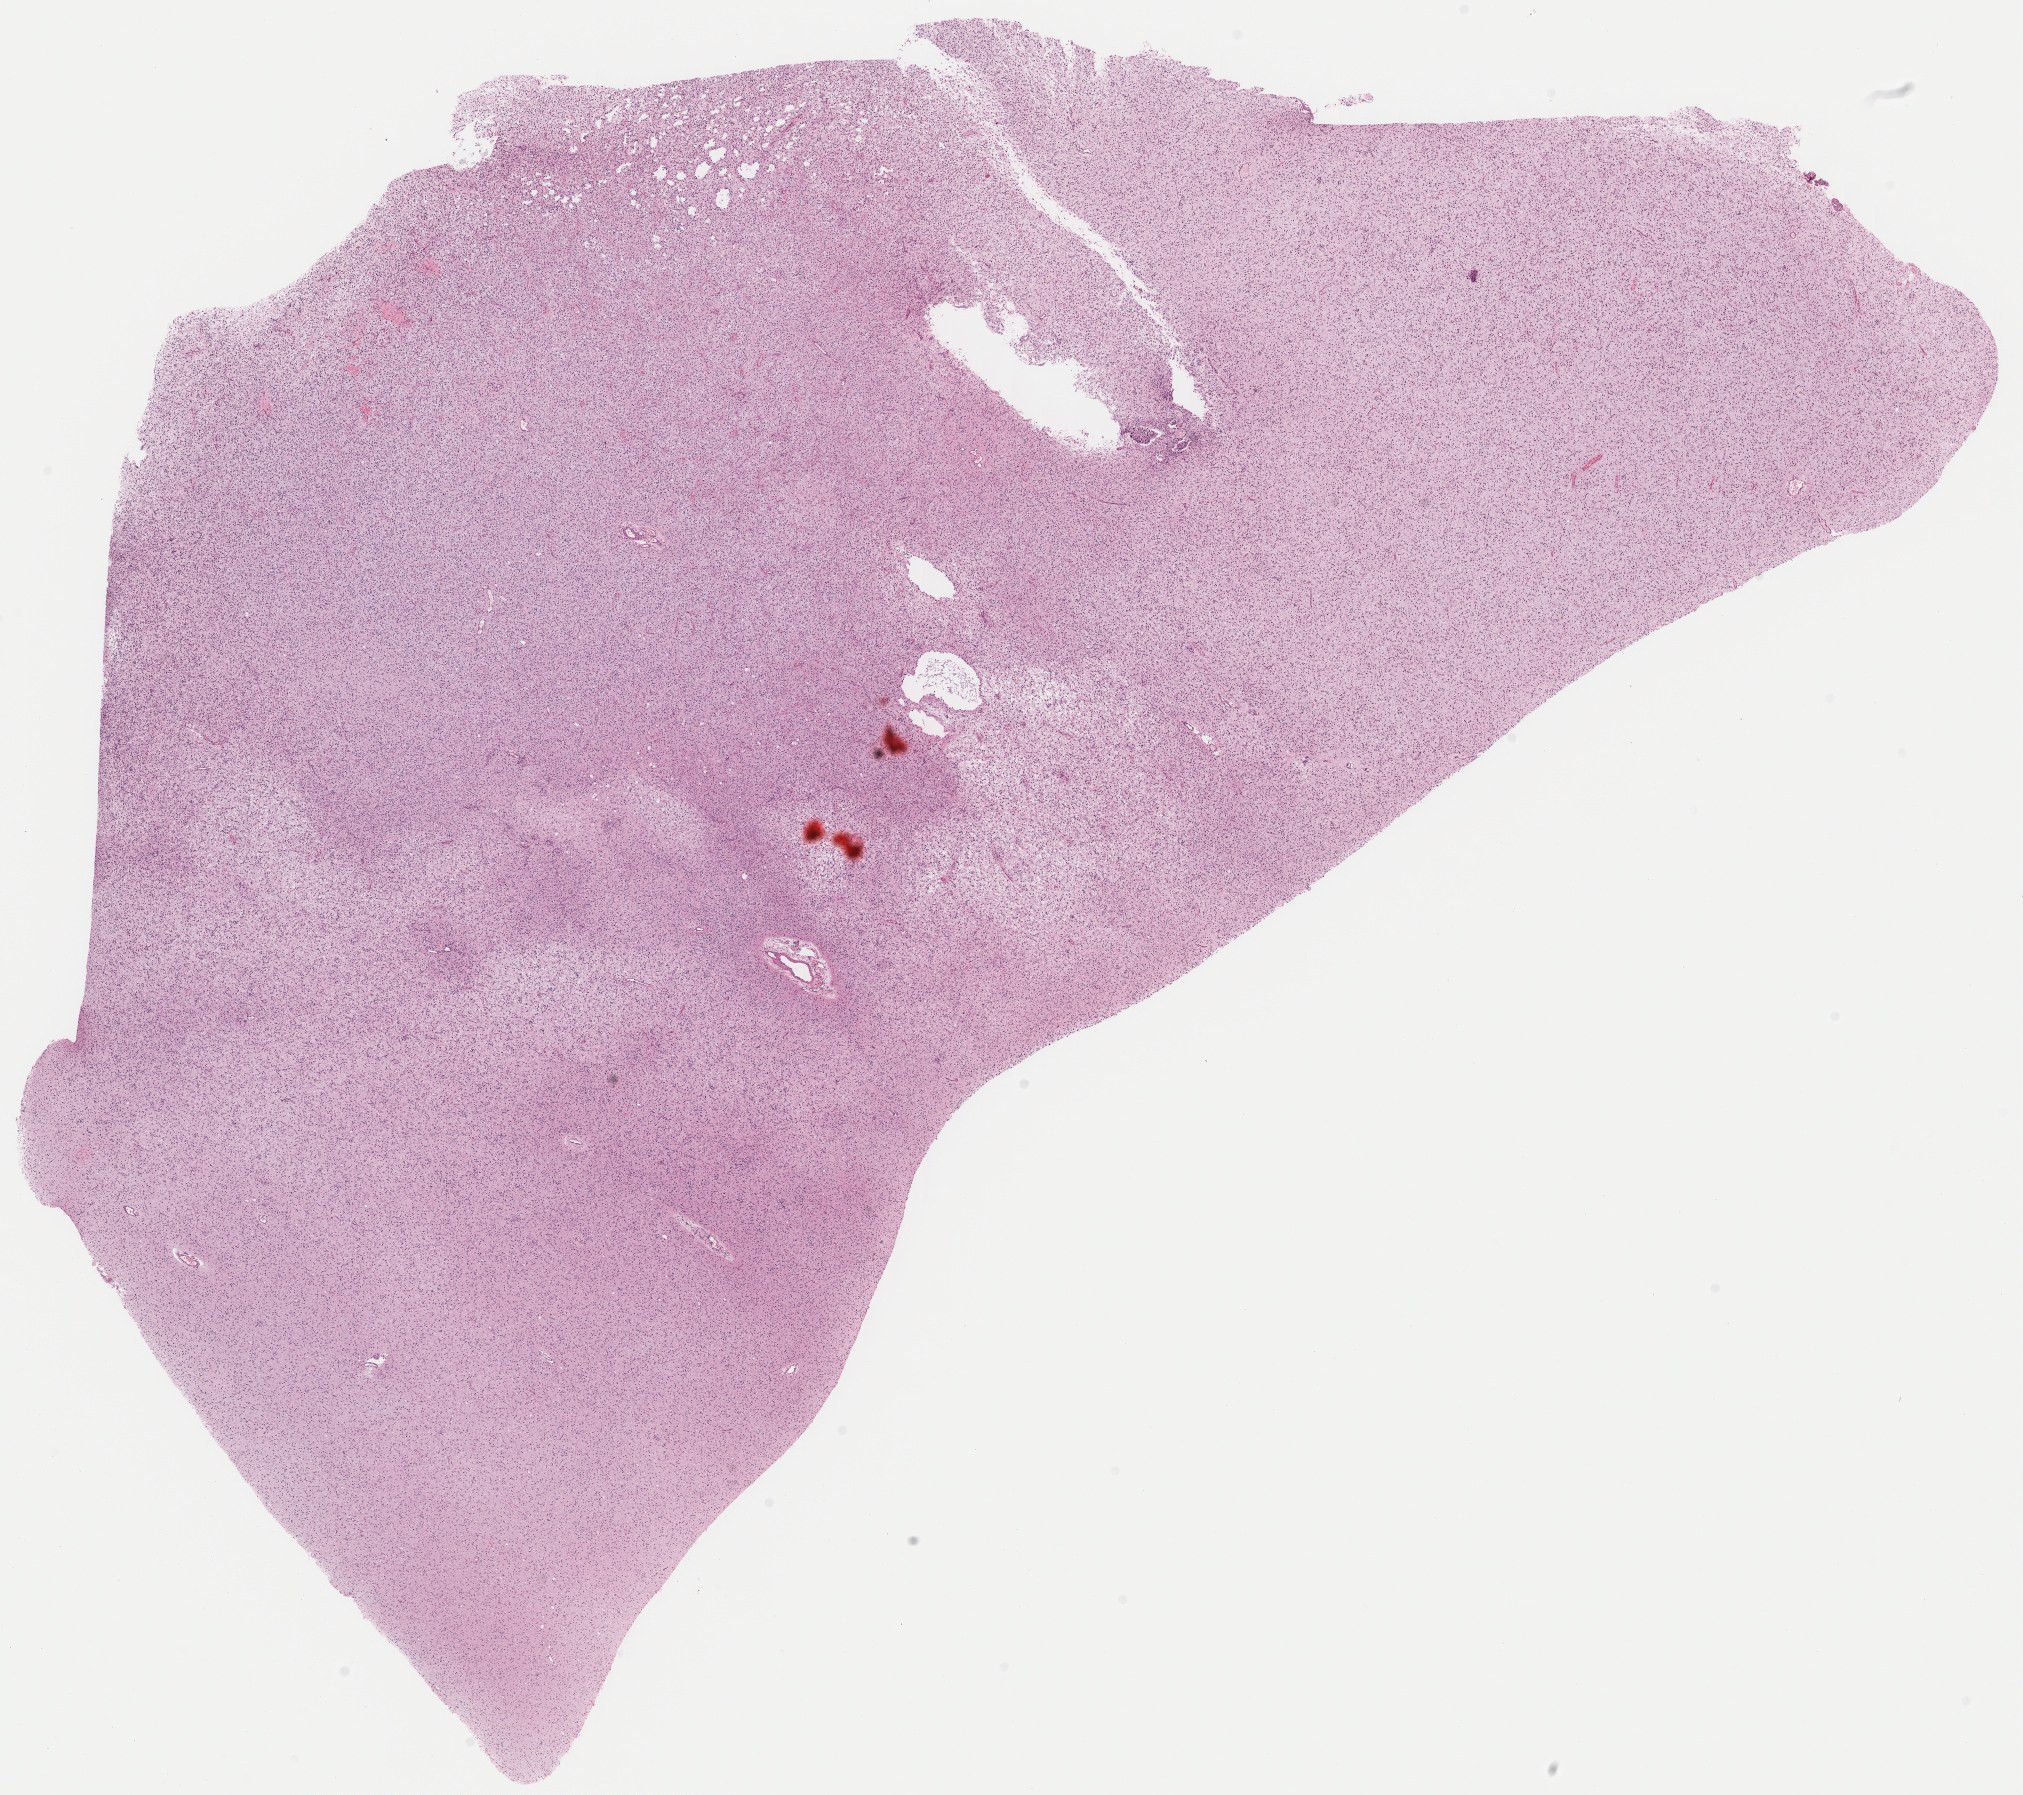
H&E whole-slide image, shown as a low-resolution overview of the whole scanned area (about 15.9 x 14.1 mm, from a 40x scan), FFPE section, sample: primary tumour, brain. Male patient; age at initial diagnosis 26 years.
Pathologic diagnosis: Mixed glioma.